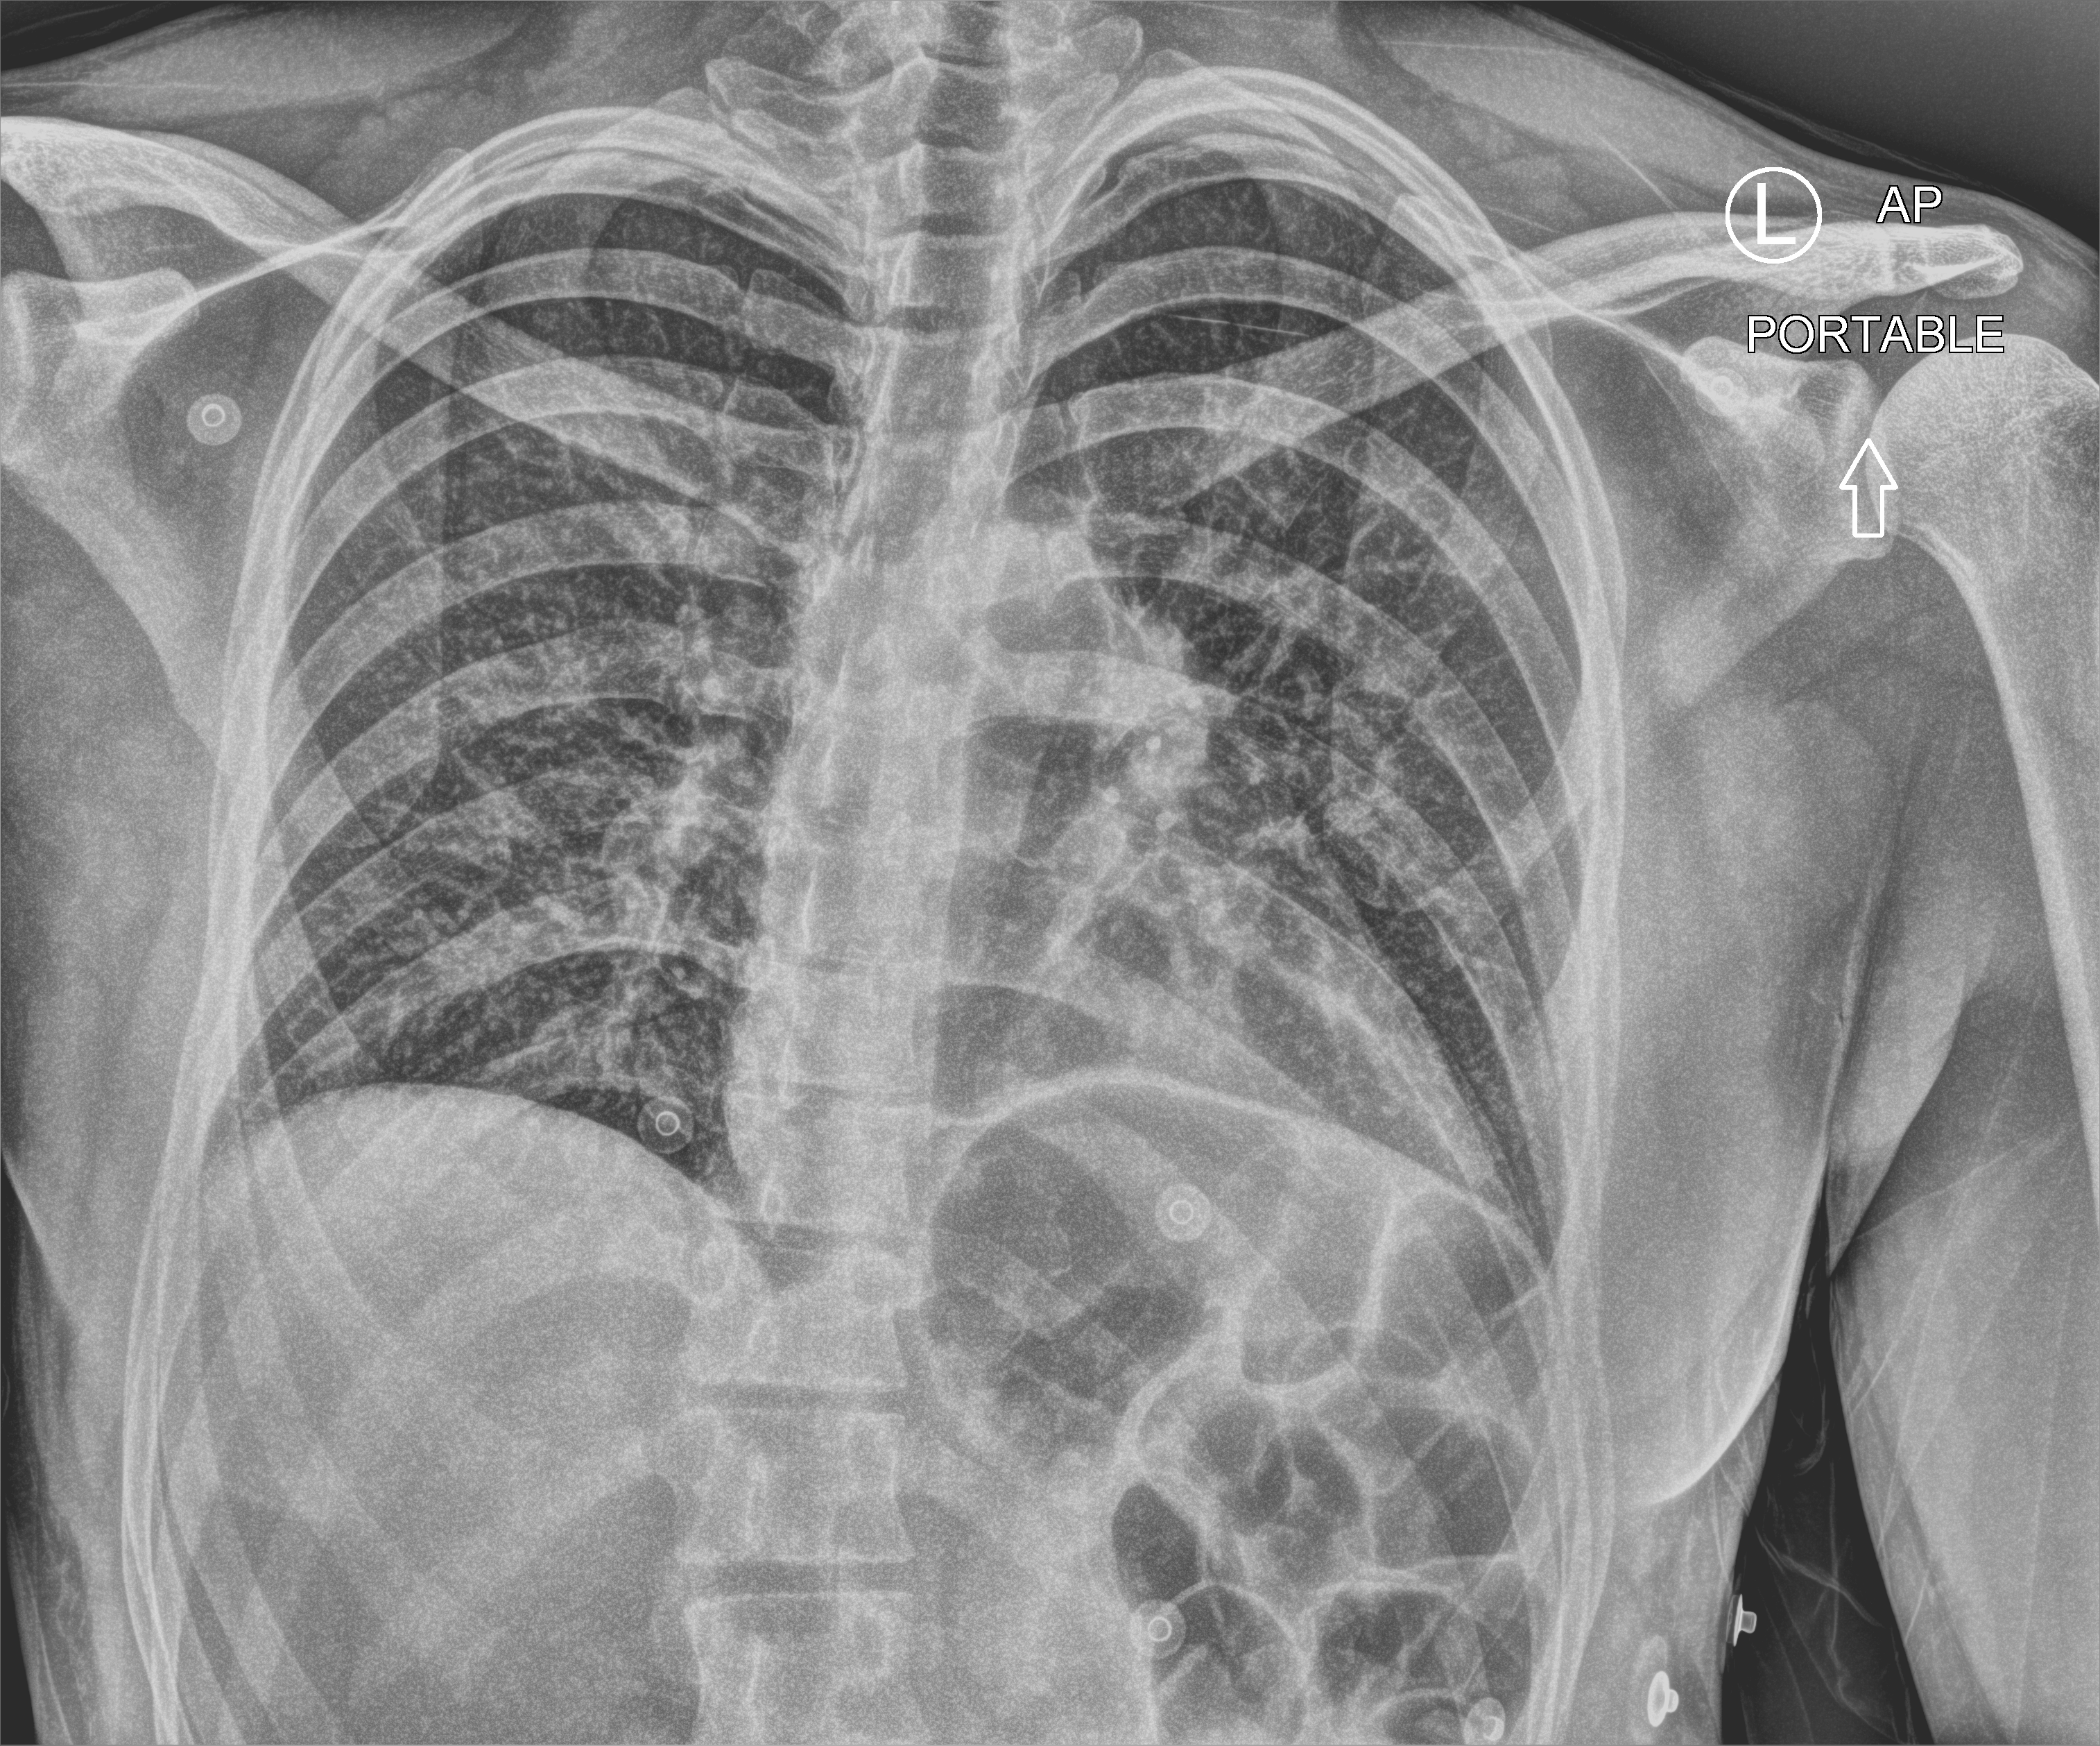
Bedside chest radiograph (computed radiography), anteroposterior (AP) projection. Male patient hospitalised with COVID-19, age 18–59 years.
Hospital-stay facts (about this admission, not read from this image; timing relative to this image not recorded): mechanically ventilated during this hospital stay: no.